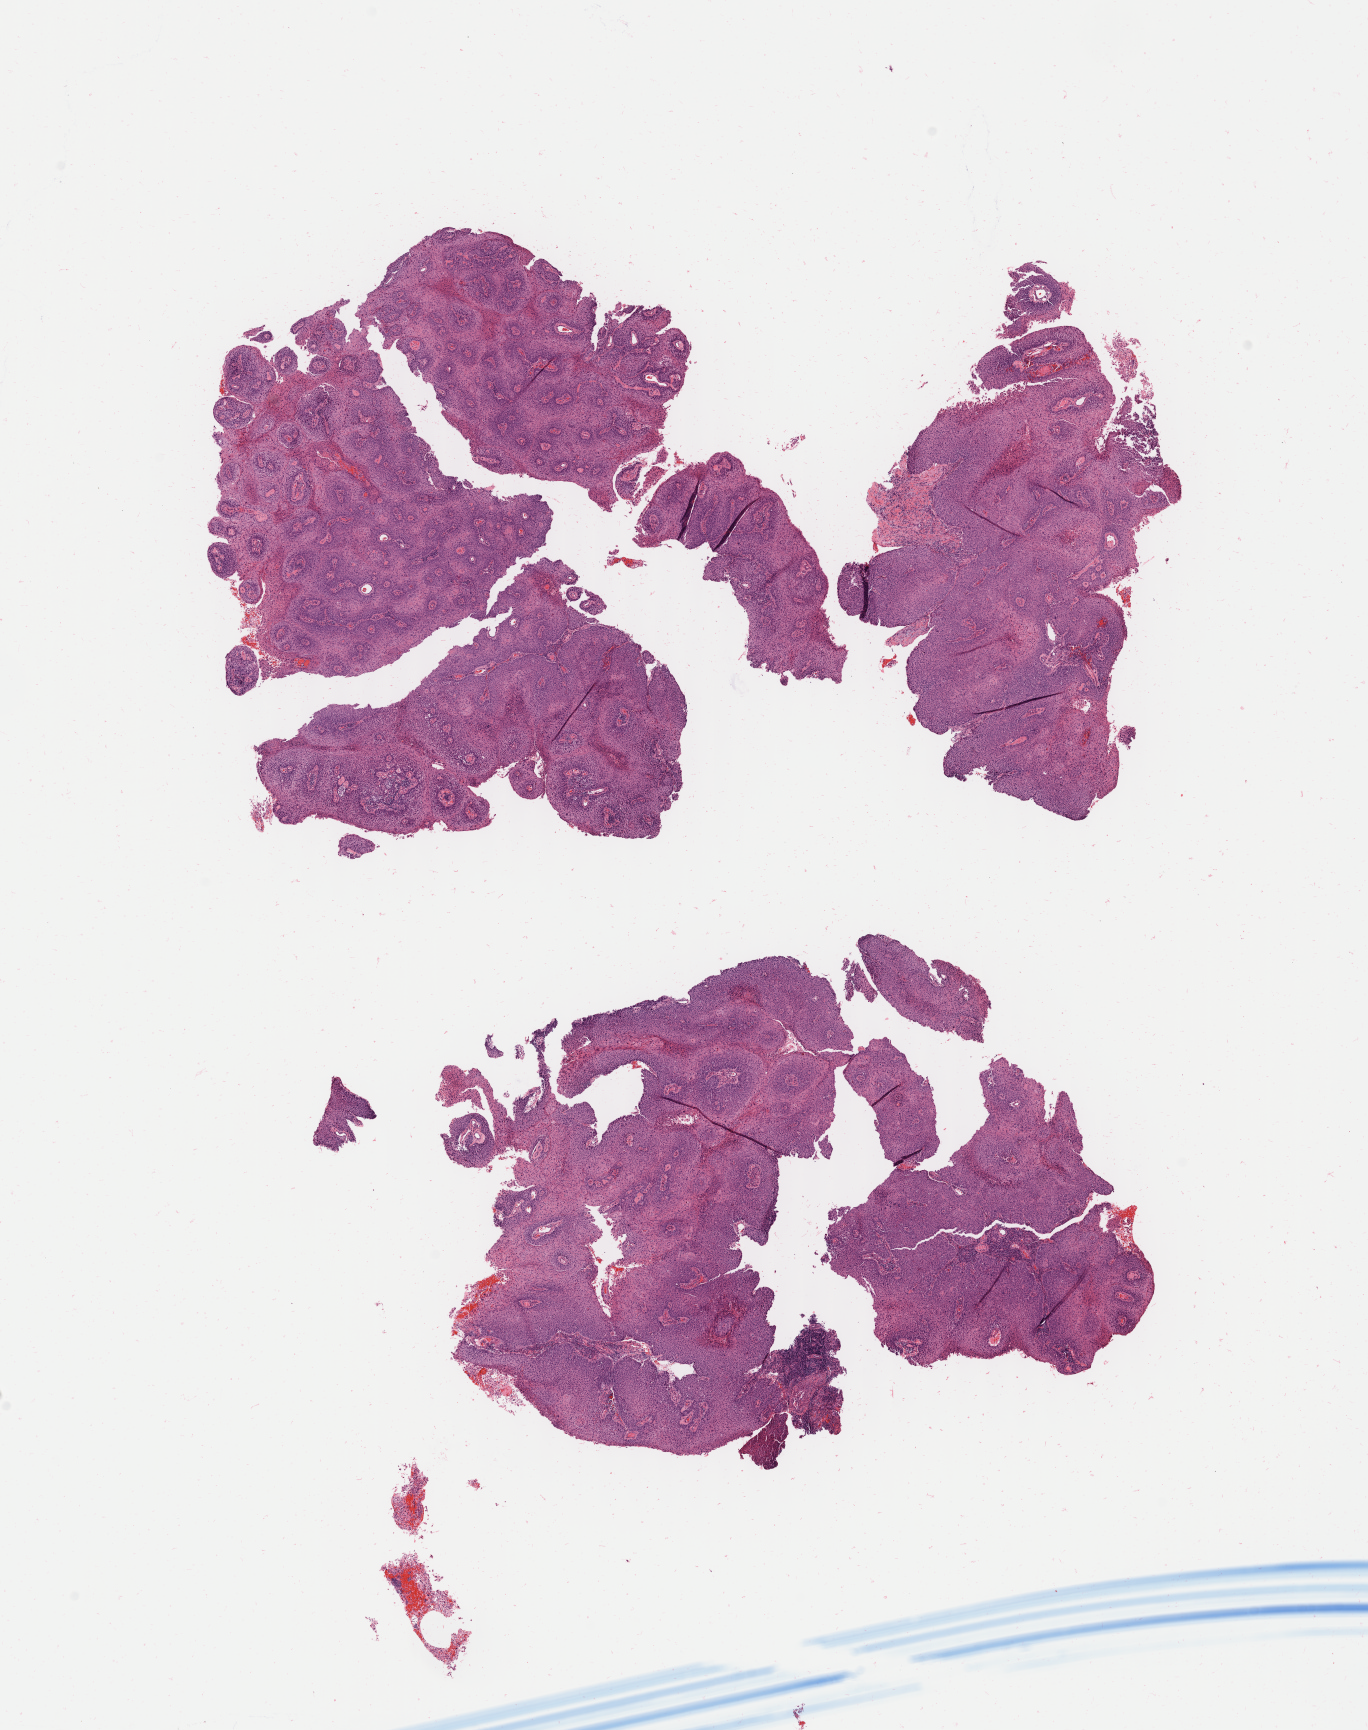
H&E whole-slide image — low-resolution overview of the scanned area, about 10.9 x 13.8 mm, tumor tissue, anatomic site: cervix. Patient: female, age 45 years.
Histologic diagnosis: Squamous cell carcinoma, keratinizing, NOS.